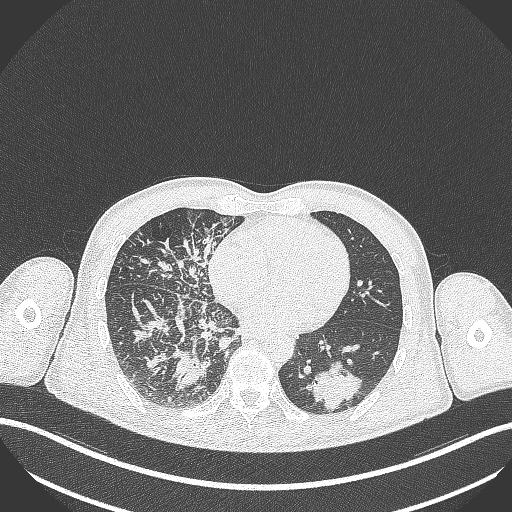
Chest CT, one axial slice; reconstruction kernel B70f; 120 kVp; lung window (W 1500 / L -600 HU); 1 mm slice thickness; 512 × 512 image matrix, field of view 400 × 400 mm. Male patient, age 49 years. Case-level facts recorded for this patient, not image findings: clinical TNM (as recorded): T2b N1 M0.
Annotated regions visible in this slice (rectangle marked by the reading radiologist):
- lung tumour (recorded histology: adenocarcinoma): bounding box (x1, y1, x2, y2) in pixels: (305, 357, 368, 411)